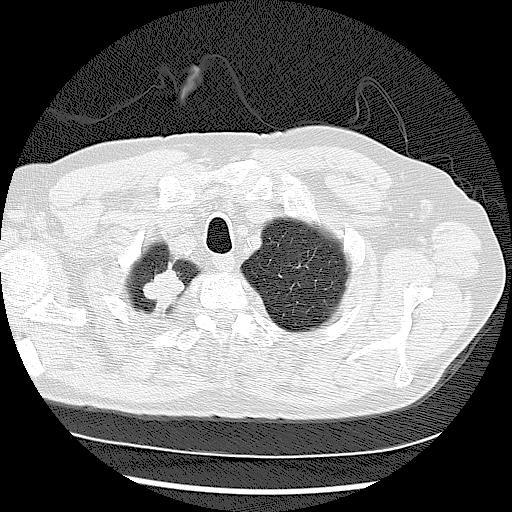
Low-dose screening chest CT, one axial slice. Slice 105 of 122 in the series (ordered by position). 120 kVp. Lung window (W 1500 / L -600 HU). 2.5 mm slice thickness. 512 × 512 image matrix, field of view 360 × 360 mm.
Annotated regions visible in this slice (expert manual segmentation):
- lesion 2 (tumor, upper lobe of right lung): bounding box <143,270,185,314> (left, top, right, bottom; pixels)